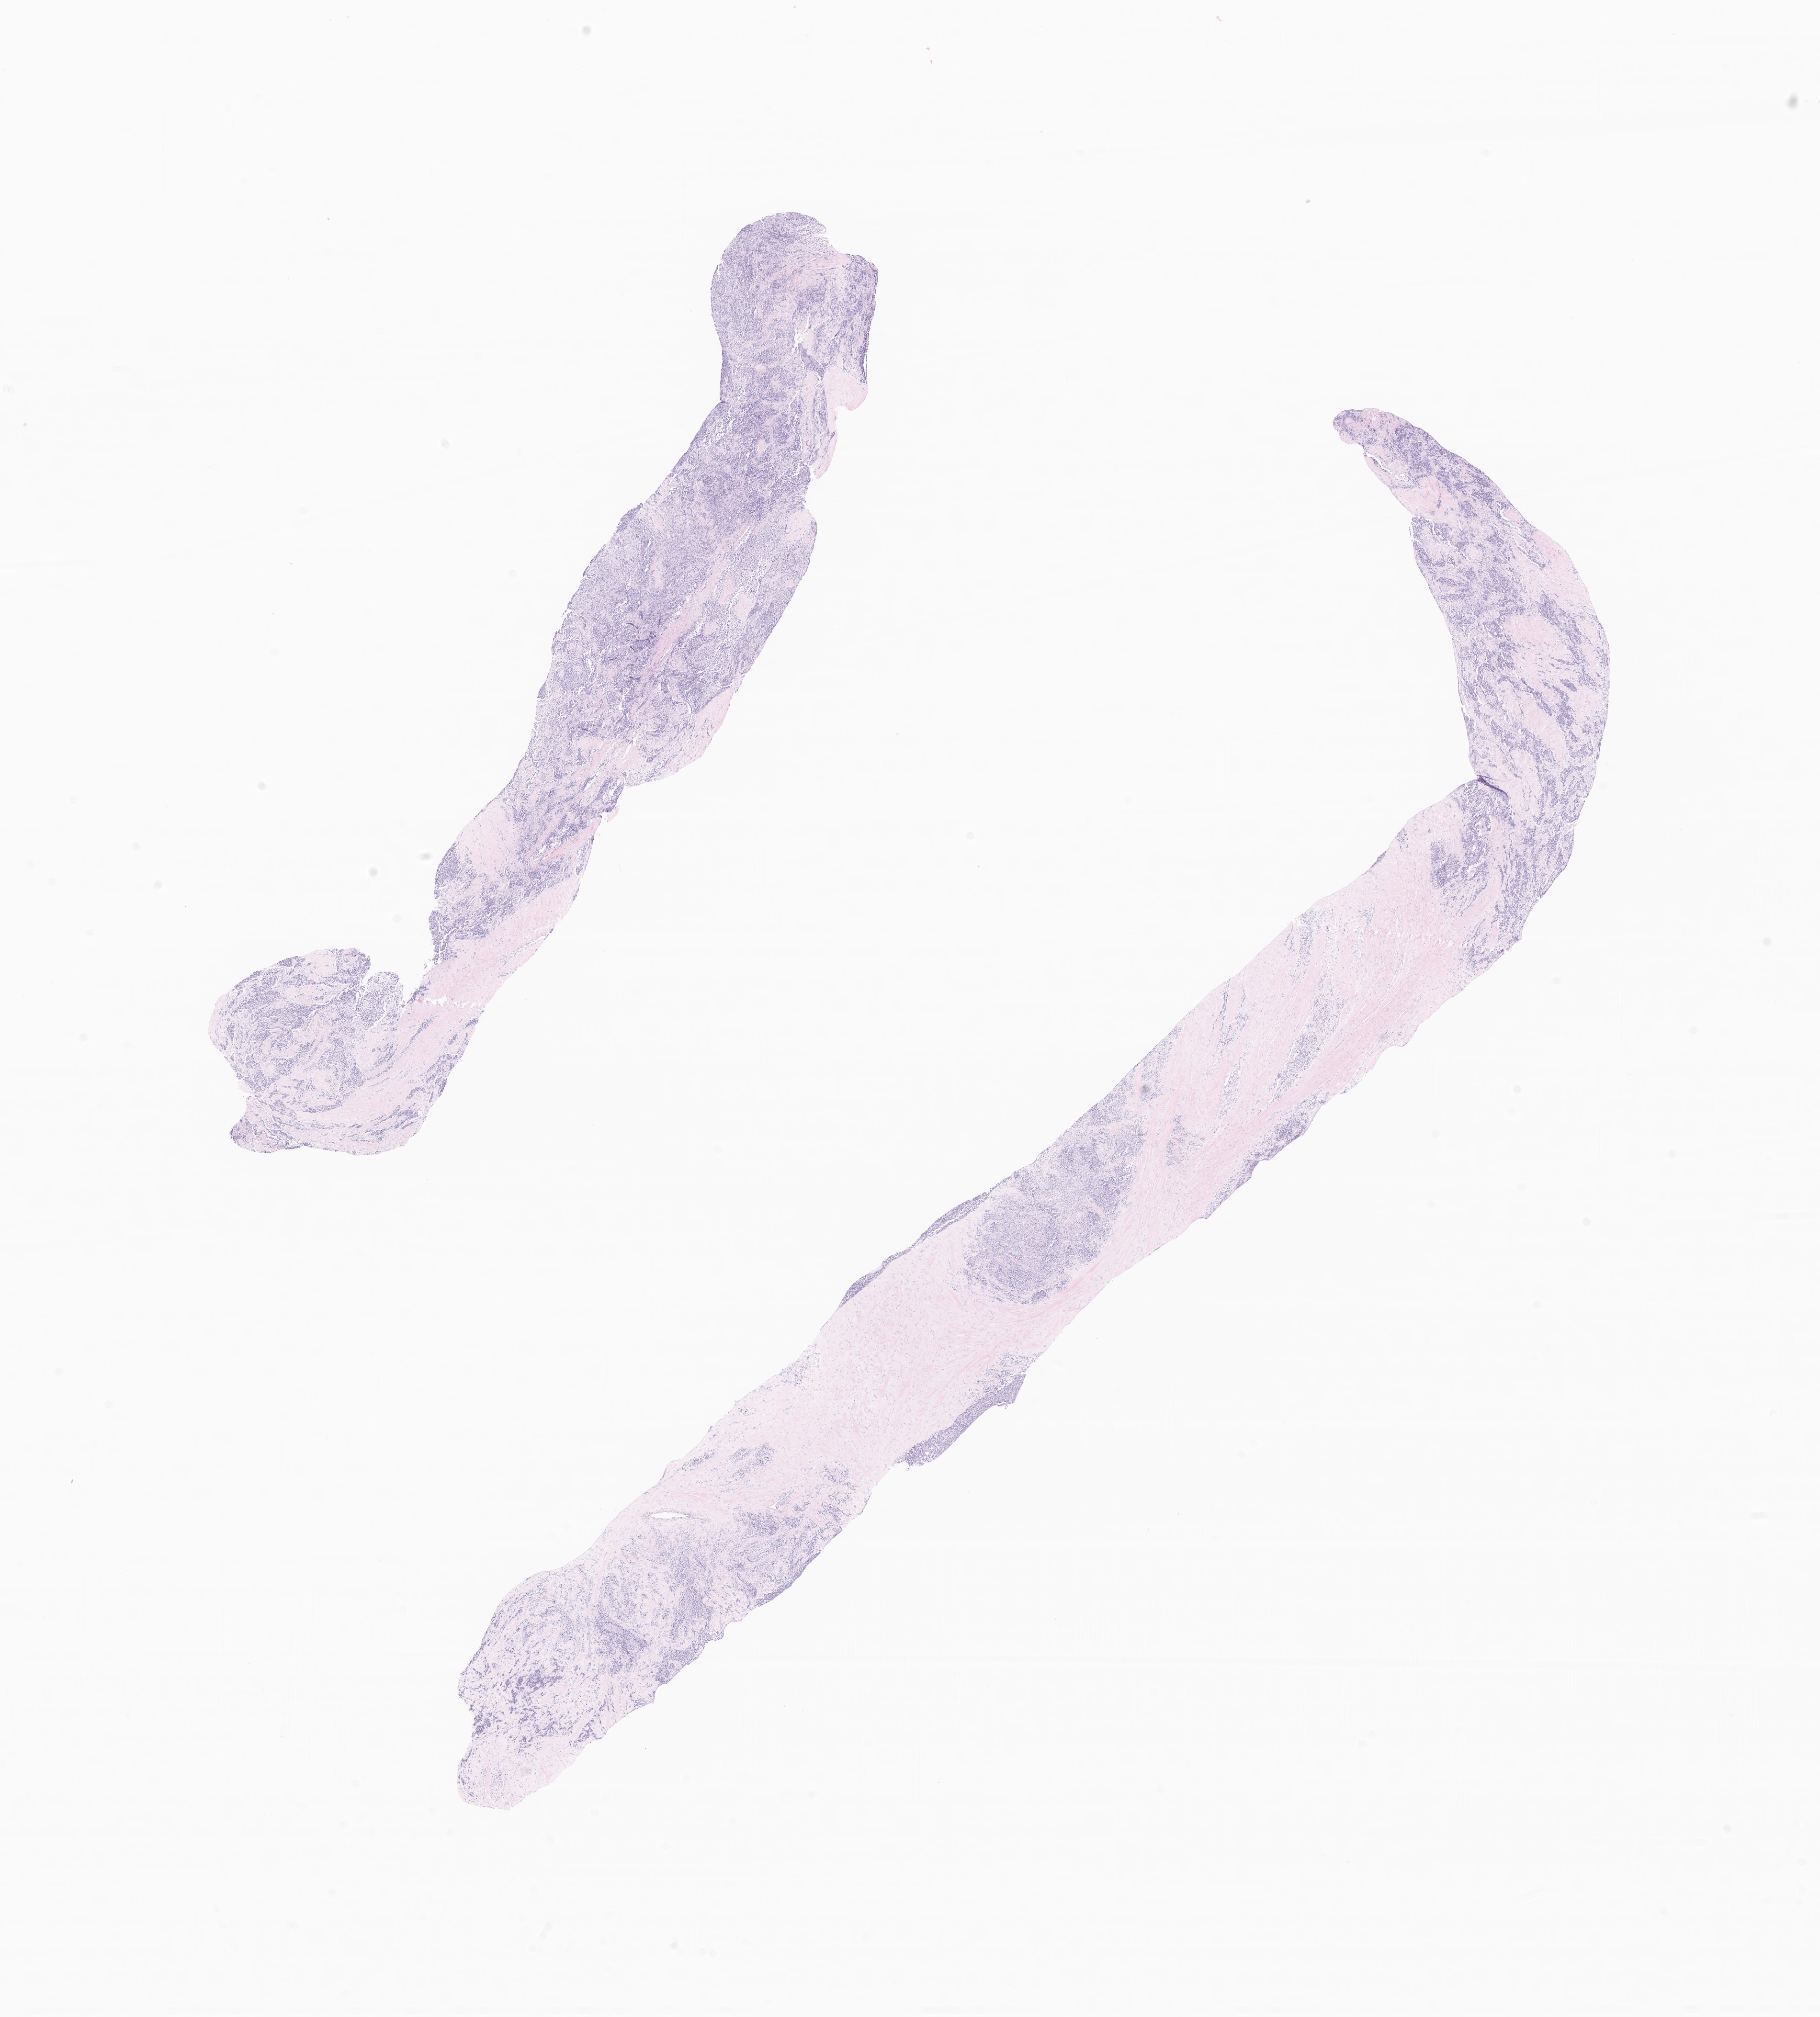
Hematoxylin and eosin (H&E) whole-slide image of tumor tissue from the lower limb, a low-resolution overview of the entire scanned area, about 16.0 x 17.8 mm. Formalin-fixed paraffin-embedded section. Female patient, age 49 months (4 years 1 month).
Diagnosis: Alveolar rhabdomyosarcoma.